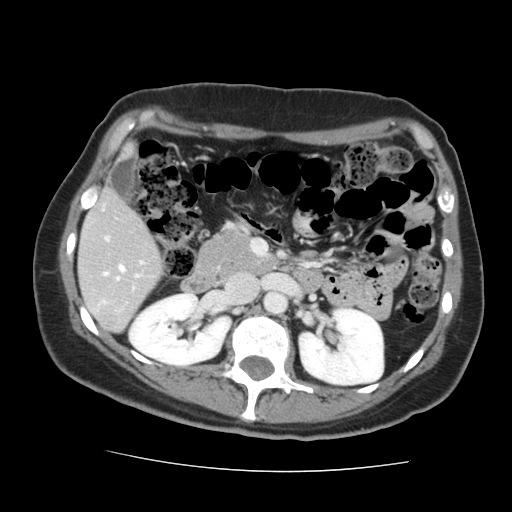
Contrast-enhanced abdominal CT, one axial slice; position 71 of 144 along the scan axis; intravenous contrast given; soft-tissue window (W 400 / L 40 HU); 2.5 mm slice thickness; 512 × 512 image matrix, field of view 333 × 333 mm. Female patient, age 46 years. From the clinical record (not read from this slice): diagnosis: colorectal cancer liver metastases, imaged before liver resection; multiple liver metastases: no; largest metastasis: 2.8 cm; disease in both lobes: no.
Structures marked on this image (manually delineated by an expert):
- liver: box from (x=79, y=192) to (x=162, y=331) px
- planned liver remnant (the part of the liver to remain after resection): (x=79, y=192)–(x=162, y=321)
- portal vein (with intrahepatic branches): (x=103, y=237)–(x=143, y=280)